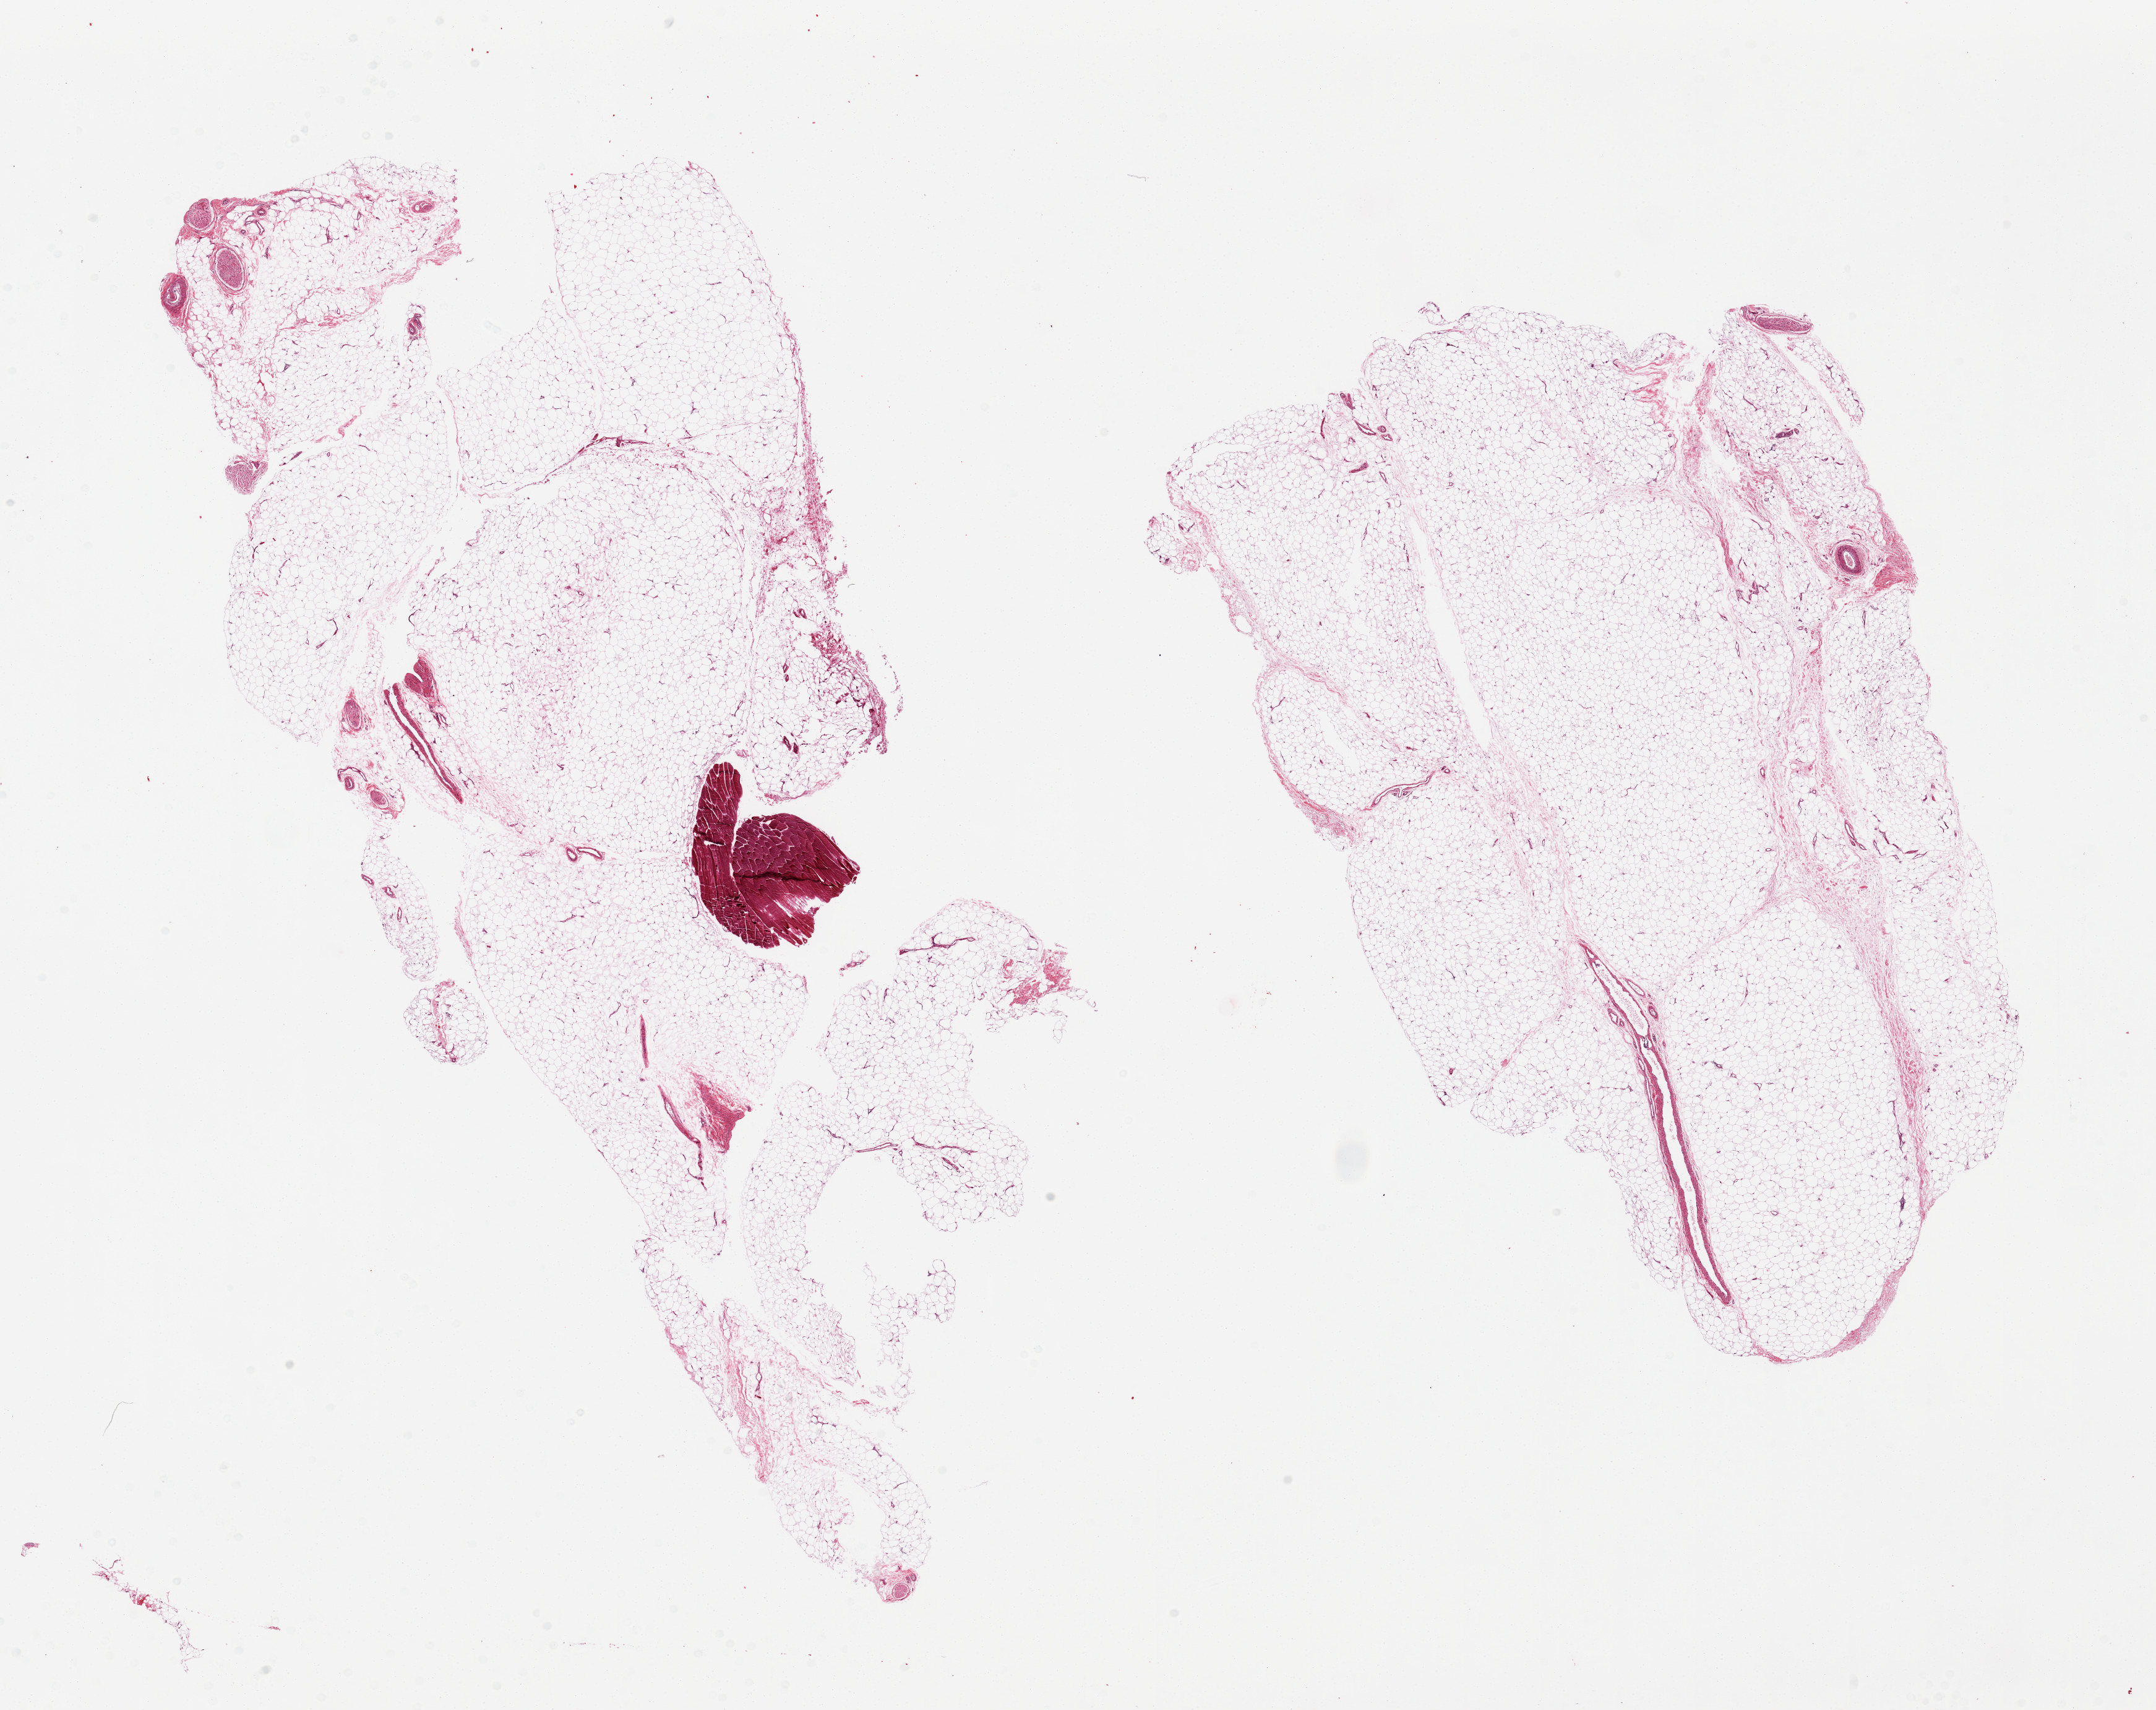
H&E whole-slide image, brightfield, a low-resolution overview of the entire scanned area, about 27.6 x 21.9 mm. PAXgene-fixed, paraffin-embedded tissue. Target tissue: adipose tissue. Tissue donor sample. Donor sex: male.
Review note (as recorded): 2 pieces, includes small portion of nerve, detached fragment of skeletal muscle abuts one piece of fat.